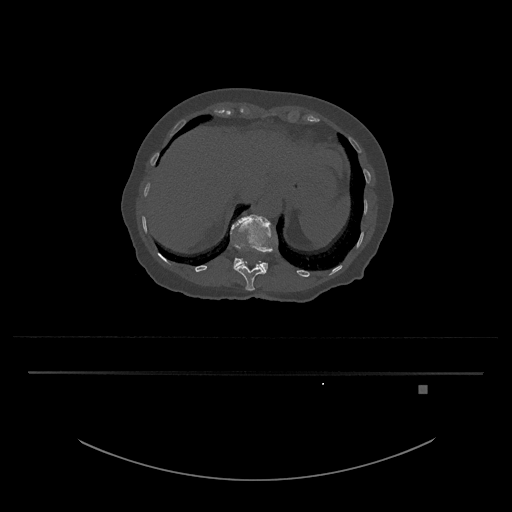
CT including the spine, one axial slice; position 587 of 797 along the scan axis; 120 kVp; bone window (W 1800 / L 400 HU); 0.5 mm slice thickness; 512 × 512 image matrix, field of view 500 × 500 mm. Female patient, age 57 years. From the clinical record (not read from this slice): primary cancer: cervical.
Structures marked on this image (semi-automatically segmented with operator editing):
- L1 vertebra: bounding box <230,214,278,272> (left, top, right, bottom; pixels)
- T12 vertebra: <235,261,266,291>